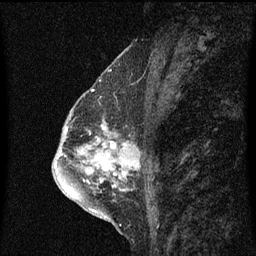
Breast MRI (dynamic contrast-enhanced), one sagittal slice. Position 31 of 60 along the scan axis. Dynamic contrast-enhanced series, image 2 of 3 at this slice position (ordered by acquisition). 1.5 T. TE 4.2 ms, TR 8.4 ms. 256 × 256 image matrix, field of view 200 × 200 mm. Patient: female, 57 years. From the clinical record (not read from this slice): setting: breast cancer imaged before/during neoadjuvant chemotherapy; receptor status: HR-positive, HER2-negative.
Annotated regions visible in this slice (semi-automatically segmented with operator editing):
- analysis volume of interest (the breast-tissue region the enhancement analysis was run in; not a lesion): bounding box (x1, y1, x2, y2) in pixels: (90, 120, 122, 145)
- tumour enhancement mask (voxels above the 70 % enhancement threshold inside the analysis volume of interest): (103, 126, 113, 143)